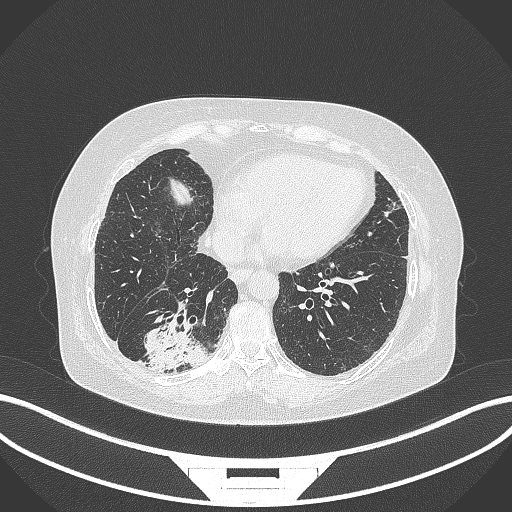
Chest CT, one axial slice; slice 72 of 296 in the series (ordered by position); reconstruction kernel B70f; 120 kVp; lung window (W 1500 / L -600 HU); 1 mm slice thickness; 512 × 512 image matrix, field of view 400 × 400 mm. Female patient, age 65 years. From the clinical record (not read from this slice): clinical TNM (as recorded): T2b N1 M0.
Outlined on this slice (rectangle marked by the reading radiologist):
- lung tumour (recorded histology: adenocarcinoma): bounding box (x1, y1, x2, y2) in pixels: (138, 322, 213, 372)